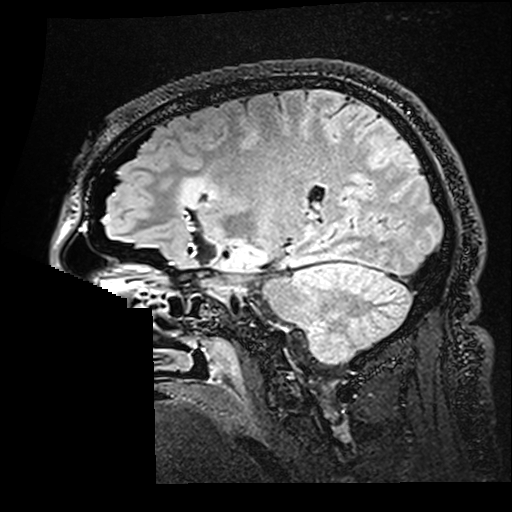
Brain MRI from a brain-tumour surgery series, one sagittal slice. Slice 110 of 176 in the series (ordered by position). T2 FLAIR. 1 mm slice thickness. 512 × 512 image matrix, field of view 250 × 250 mm. From the clinical record (not read from this slice): histopathology: Astrocytoma; WHO grade: 2; IDH mutation: yes.
Outlined on this slice (expert manual segmentation):
- residual tumour: bounding box [x1, y1, x2, y2] px = [180, 178, 220, 209]